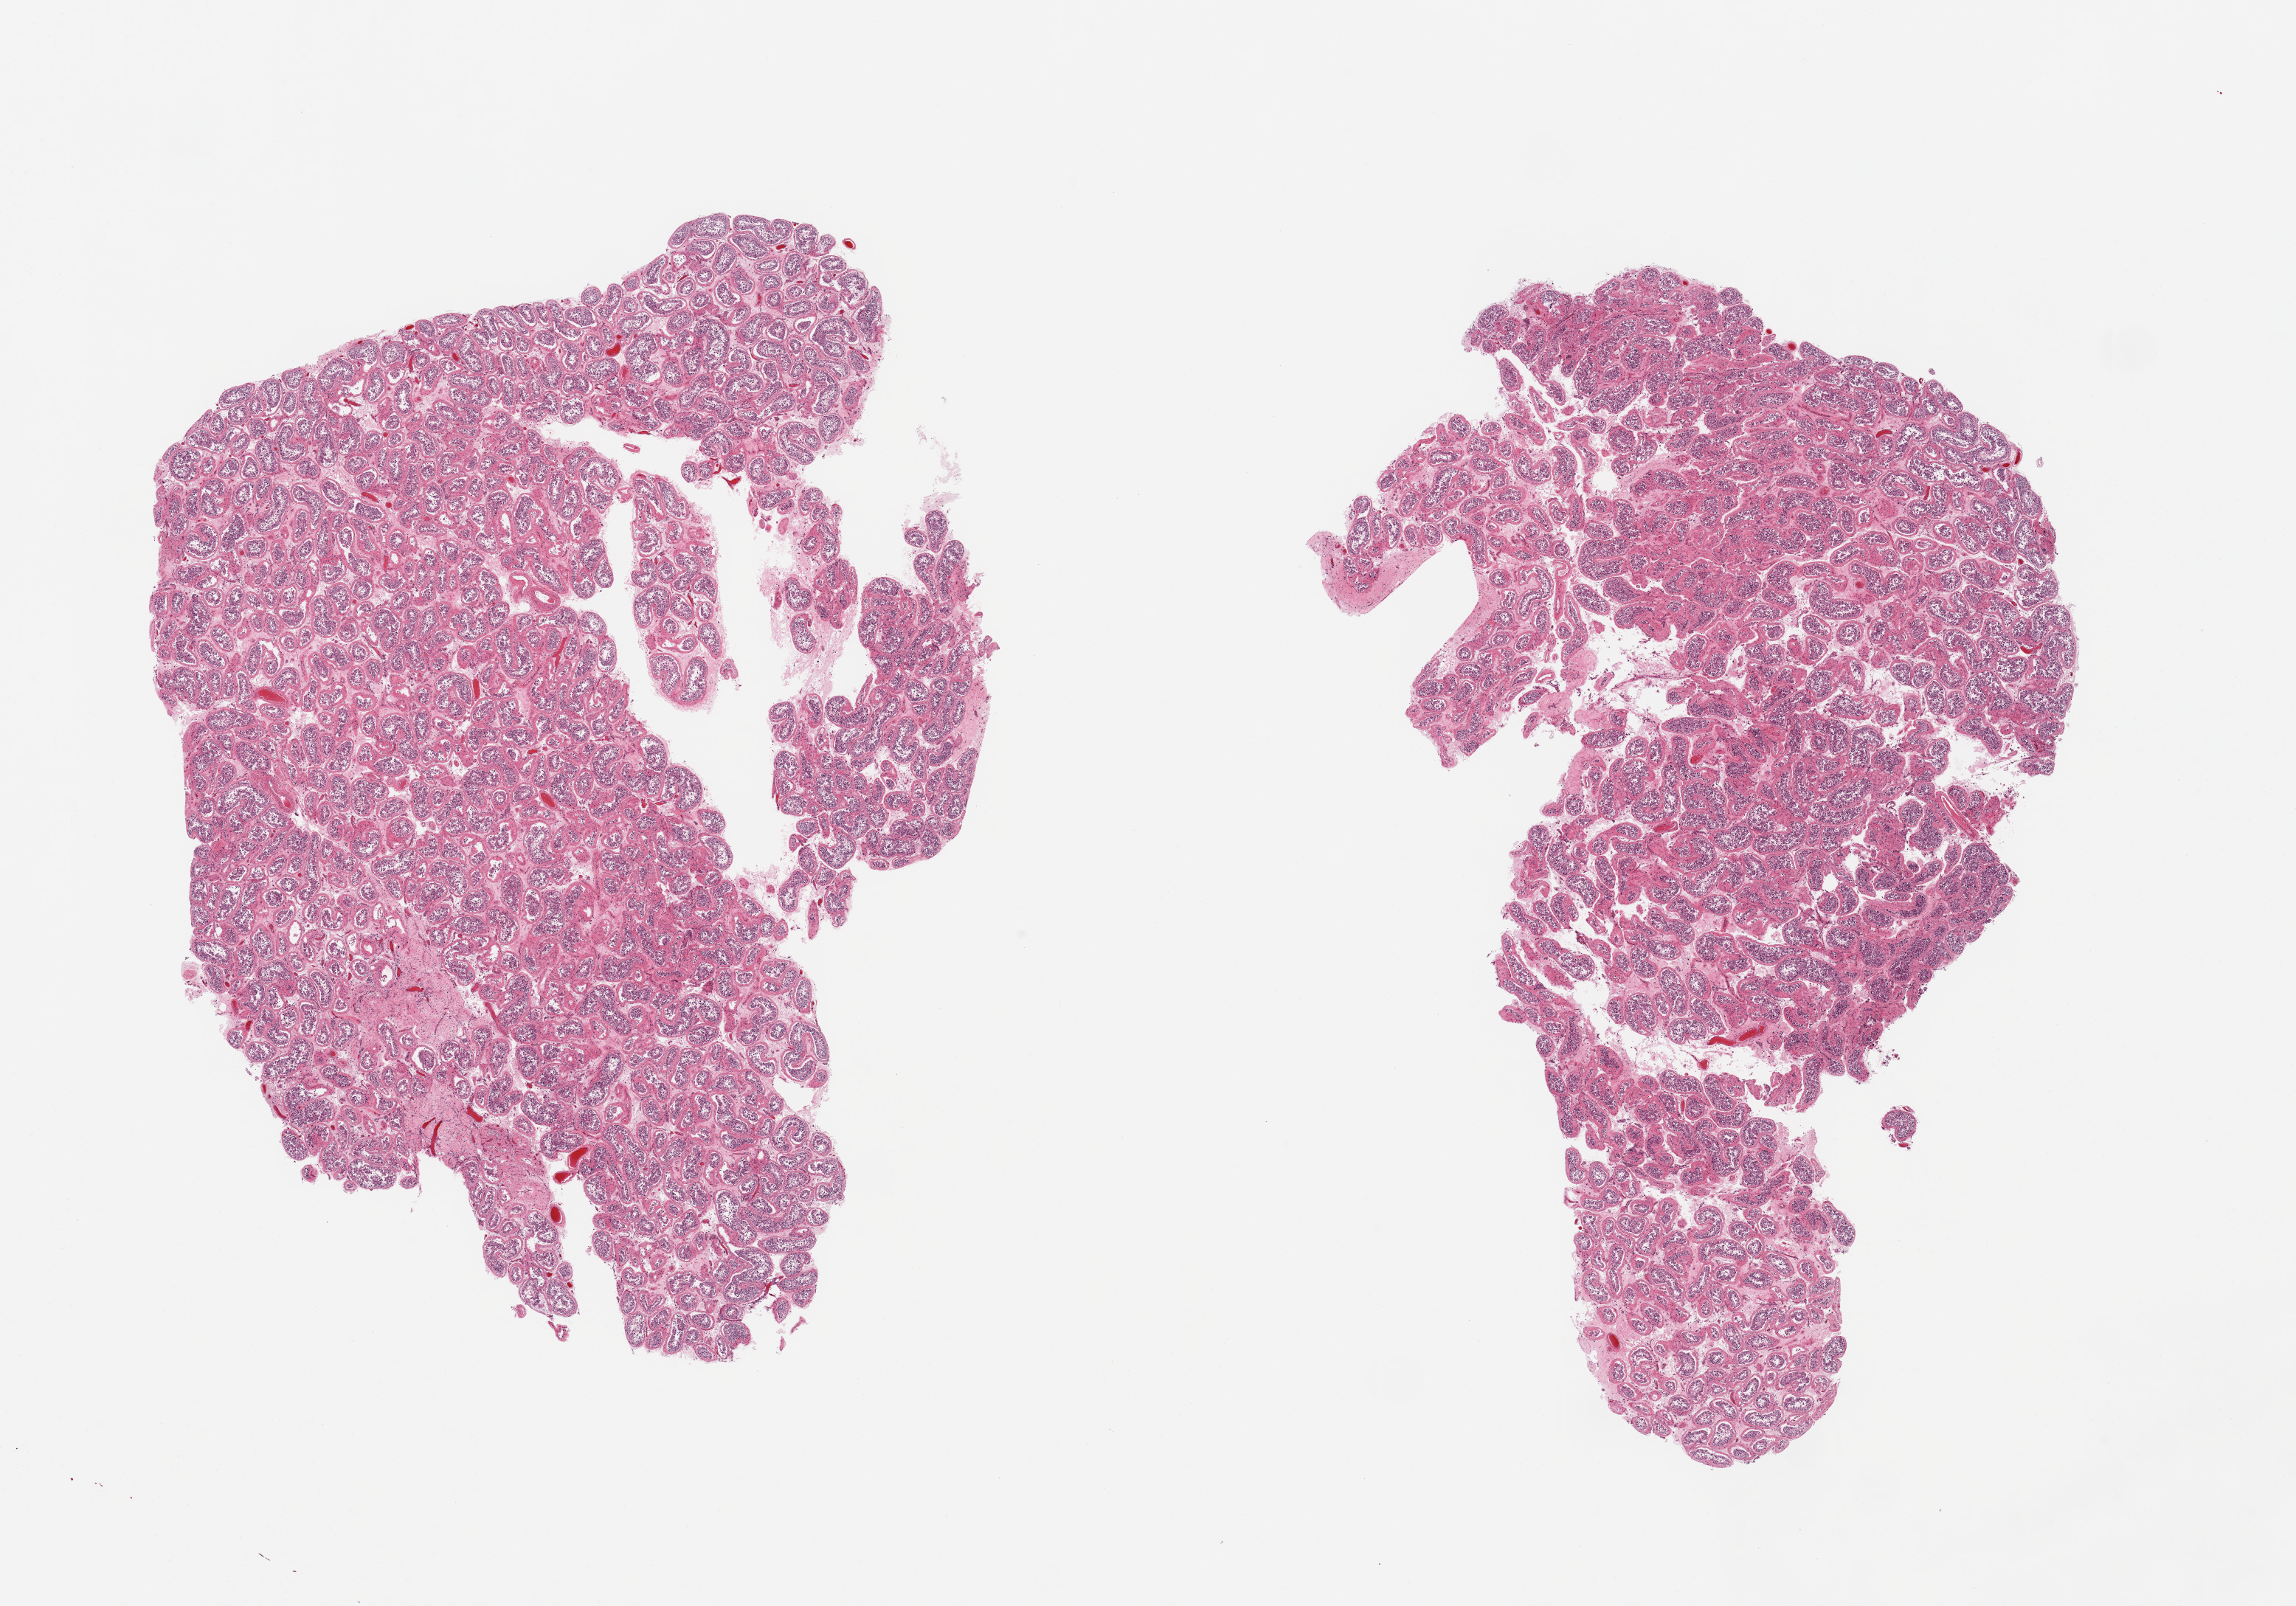
Digitized haematoxylin and eosin-stained section, brightfield — whole scanned area (about 24.6 x 17.2 mm) shown as a low-resolution overview. PAXgene-fixed, paraffin-embedded tissue. Sampled site (target tissue): testis. Donor tissue sample.
Review note (as recorded): 2 pieces, spermatogenesis appears reduced, autolyzed moderately advanced.